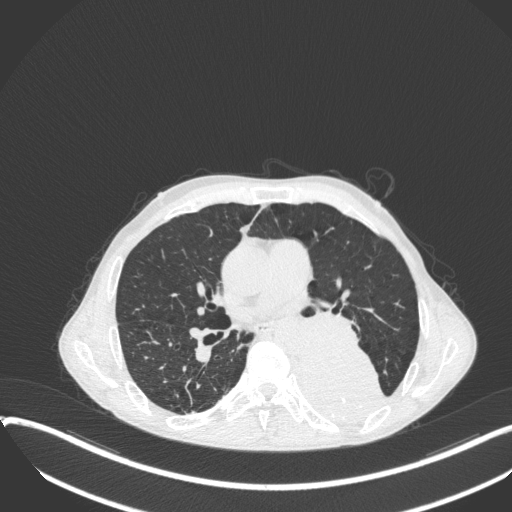
Chest CT, one axial slice. Position 200 of 400 along the scan axis. Reconstruction kernel B31f. 120 kVp. Lung window (W 1500 / L -600 HU). 1 mm slice thickness. 512 × 512 image matrix, field of view 400 × 400 mm. Patient: male, 57 years. From the clinical record (not read from this slice): clinical TNM (as recorded): T4 N0 M0.
Outlined on this slice (bounding box drawn by a radiologist):
- lung tumour (recorded histology: squamous cell carcinoma): box from (x=286, y=339) to (x=386, y=424) px